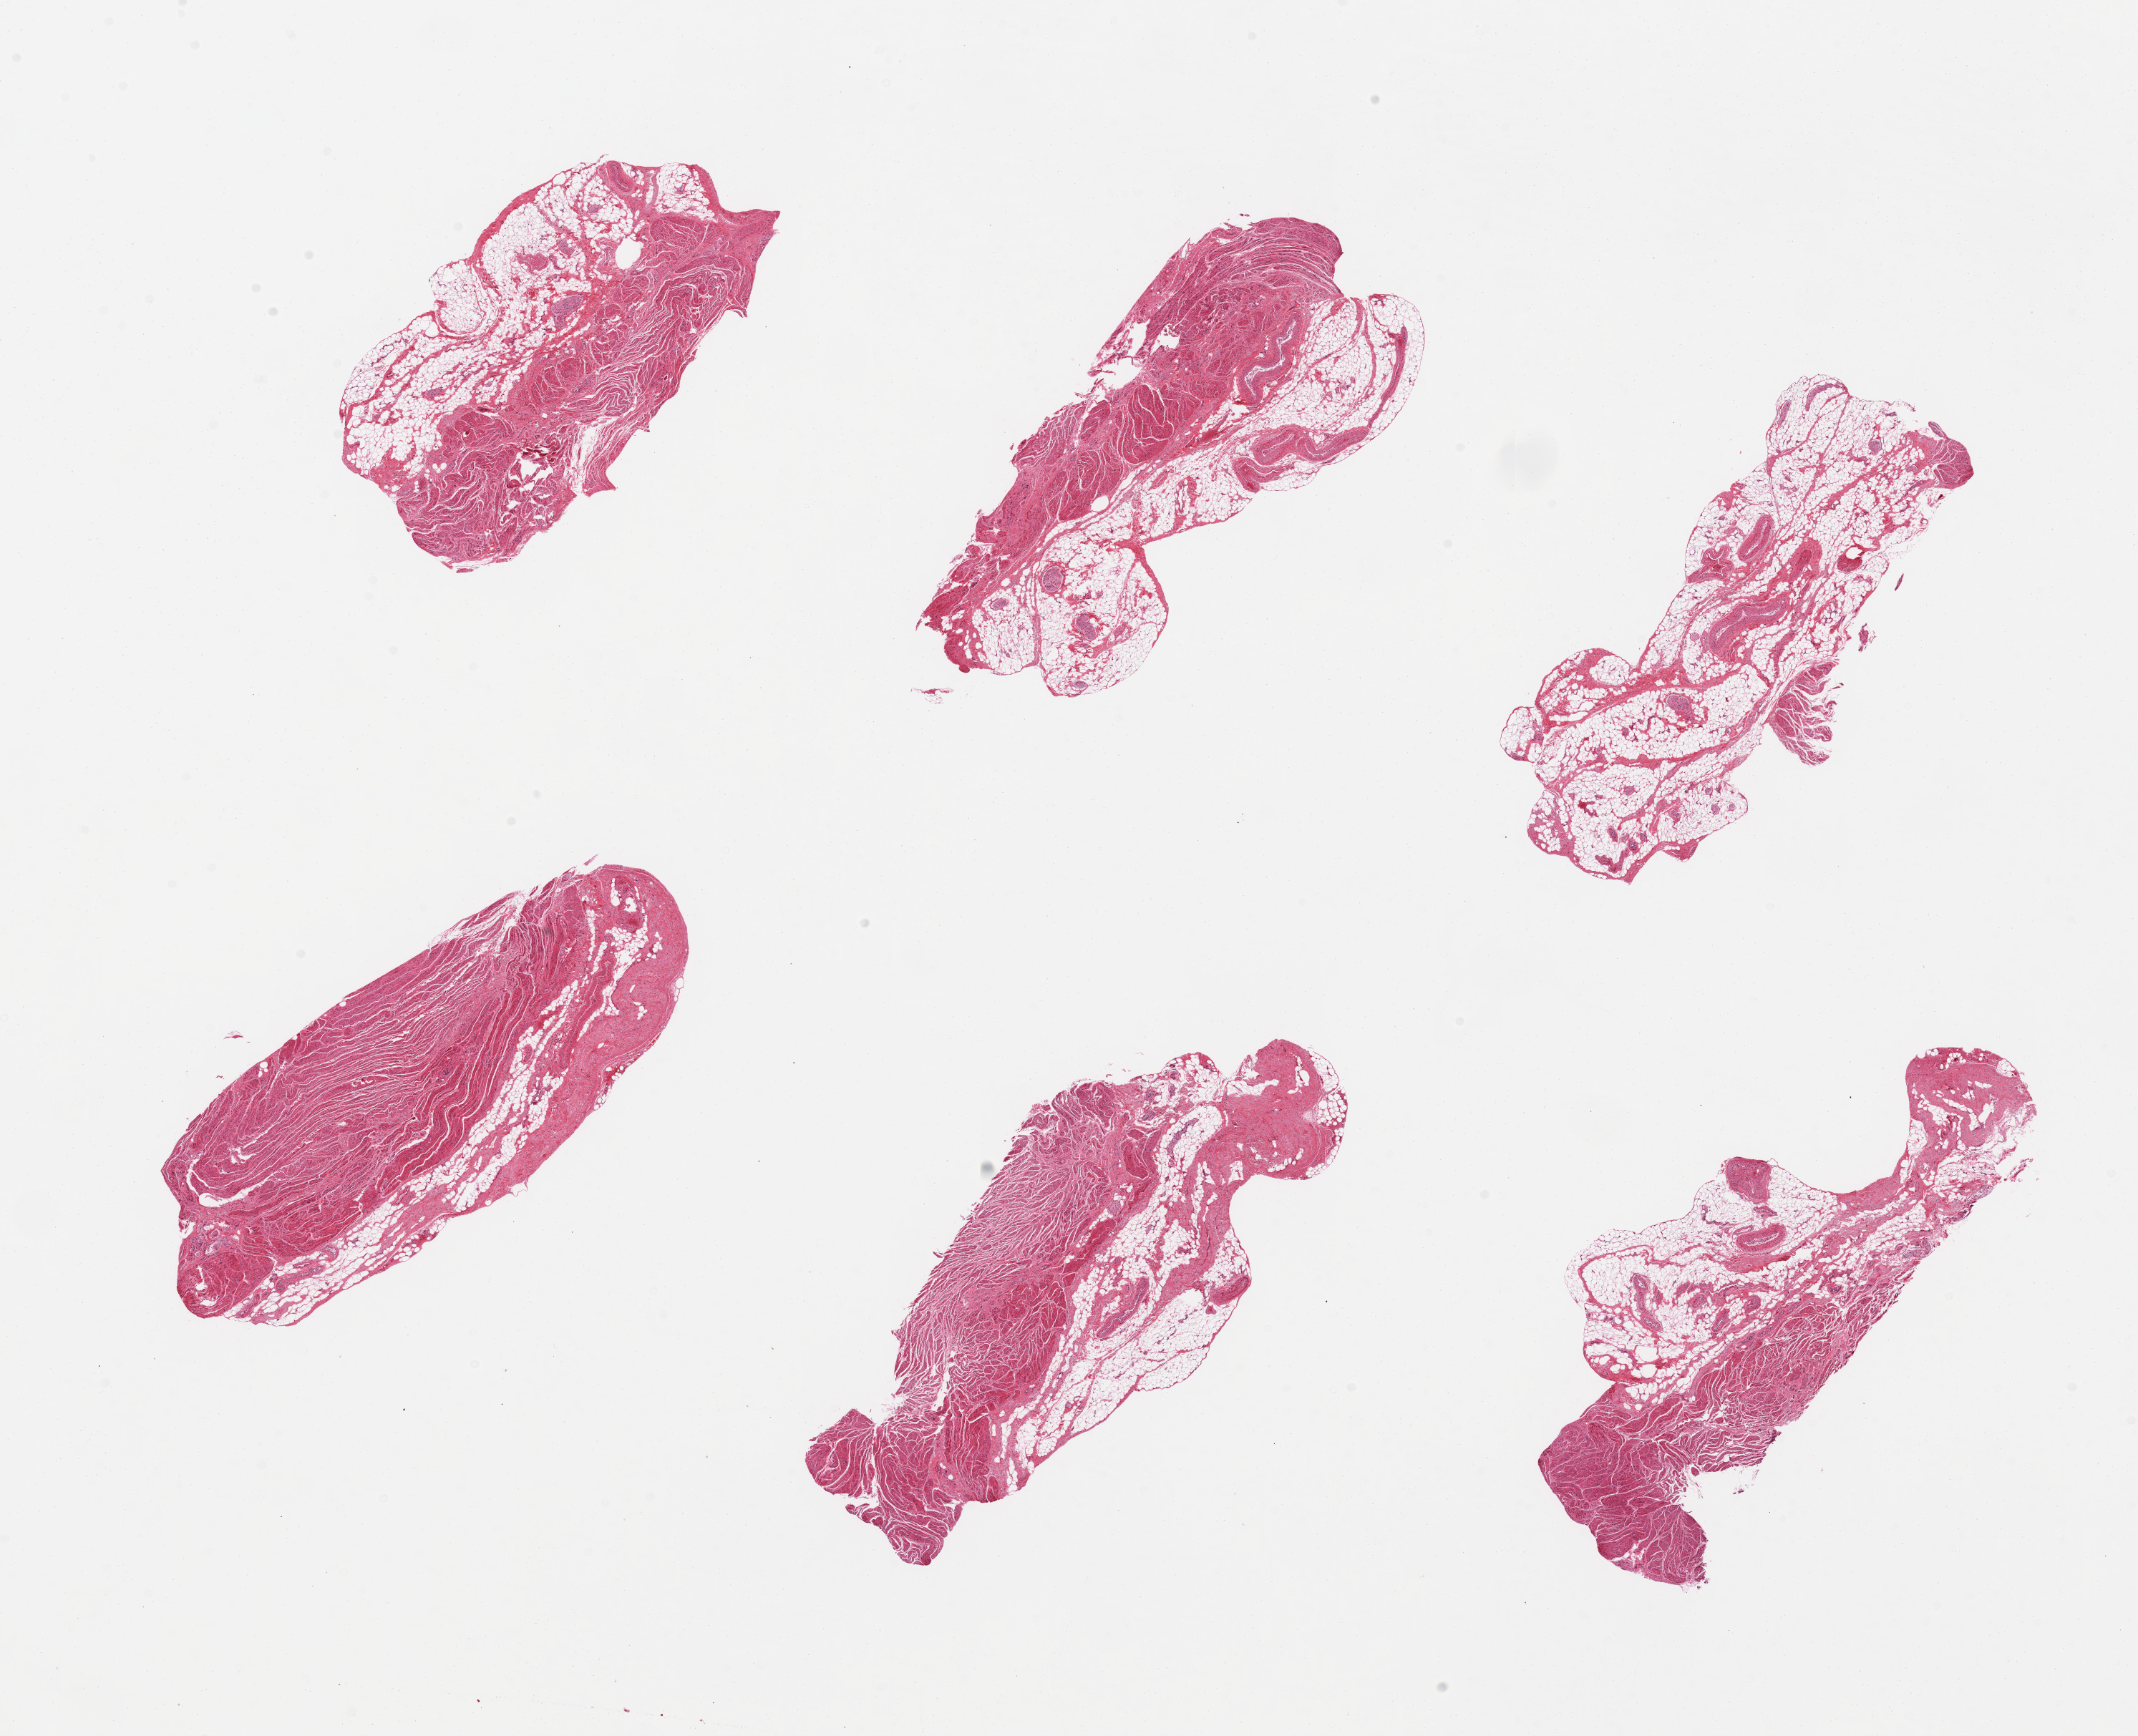
Whole-slide image, H&E stain, low-resolution overview of the scanned area, about 23.6 x 19.2 mm (acquisition: 20x scan). PAXgene-fixed, paraffin-embedded tissue. Target tissue: gastroesophageal junction. Donor tissue sample. Donor sex: male.
Pathologist's review note for this sample: 6 pieces, beware~40% adherent serosal fat.